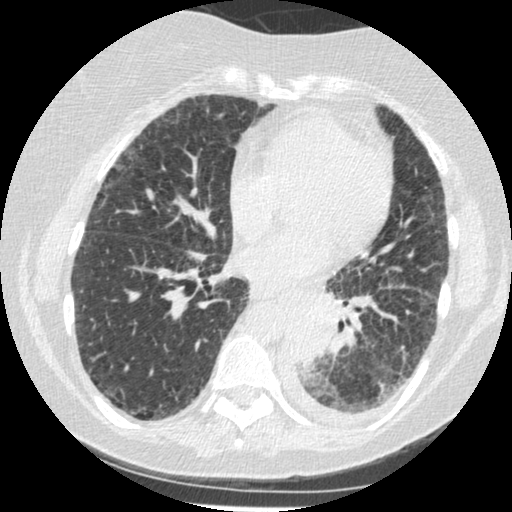
Low-dose screening chest CT, one axial slice; slice 95 of 341 in the series (ordered by position); 120 kVp; lung window (W 1500 / L -600 HU); 1.25 mm slice thickness; 512 × 512 image matrix, field of view 310 × 310 mm.
Structures marked on this image (outlined manually by an expert reader):
- lesion 1 (tumor, lower lobe of left lung): bounding box <288,310,332,365> (left, top, right, bottom; pixels)